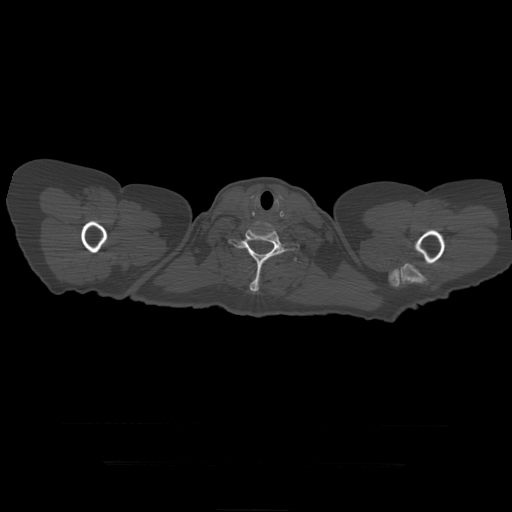
CT including the spine, one axial slice; 120 kVp; bone window (W 1800 / L 400 HU); 512 × 512 image matrix. Patient age 41 years. From the clinical record (not read from this slice): primary cancer: breast.
Annotated regions visible in this slice (semi-automatically segmented with operator editing):
- T1 vertebra: box from (x=228, y=229) to (x=300, y=292) px
- T2 vertebra: (x=295, y=259)–(x=297, y=261)